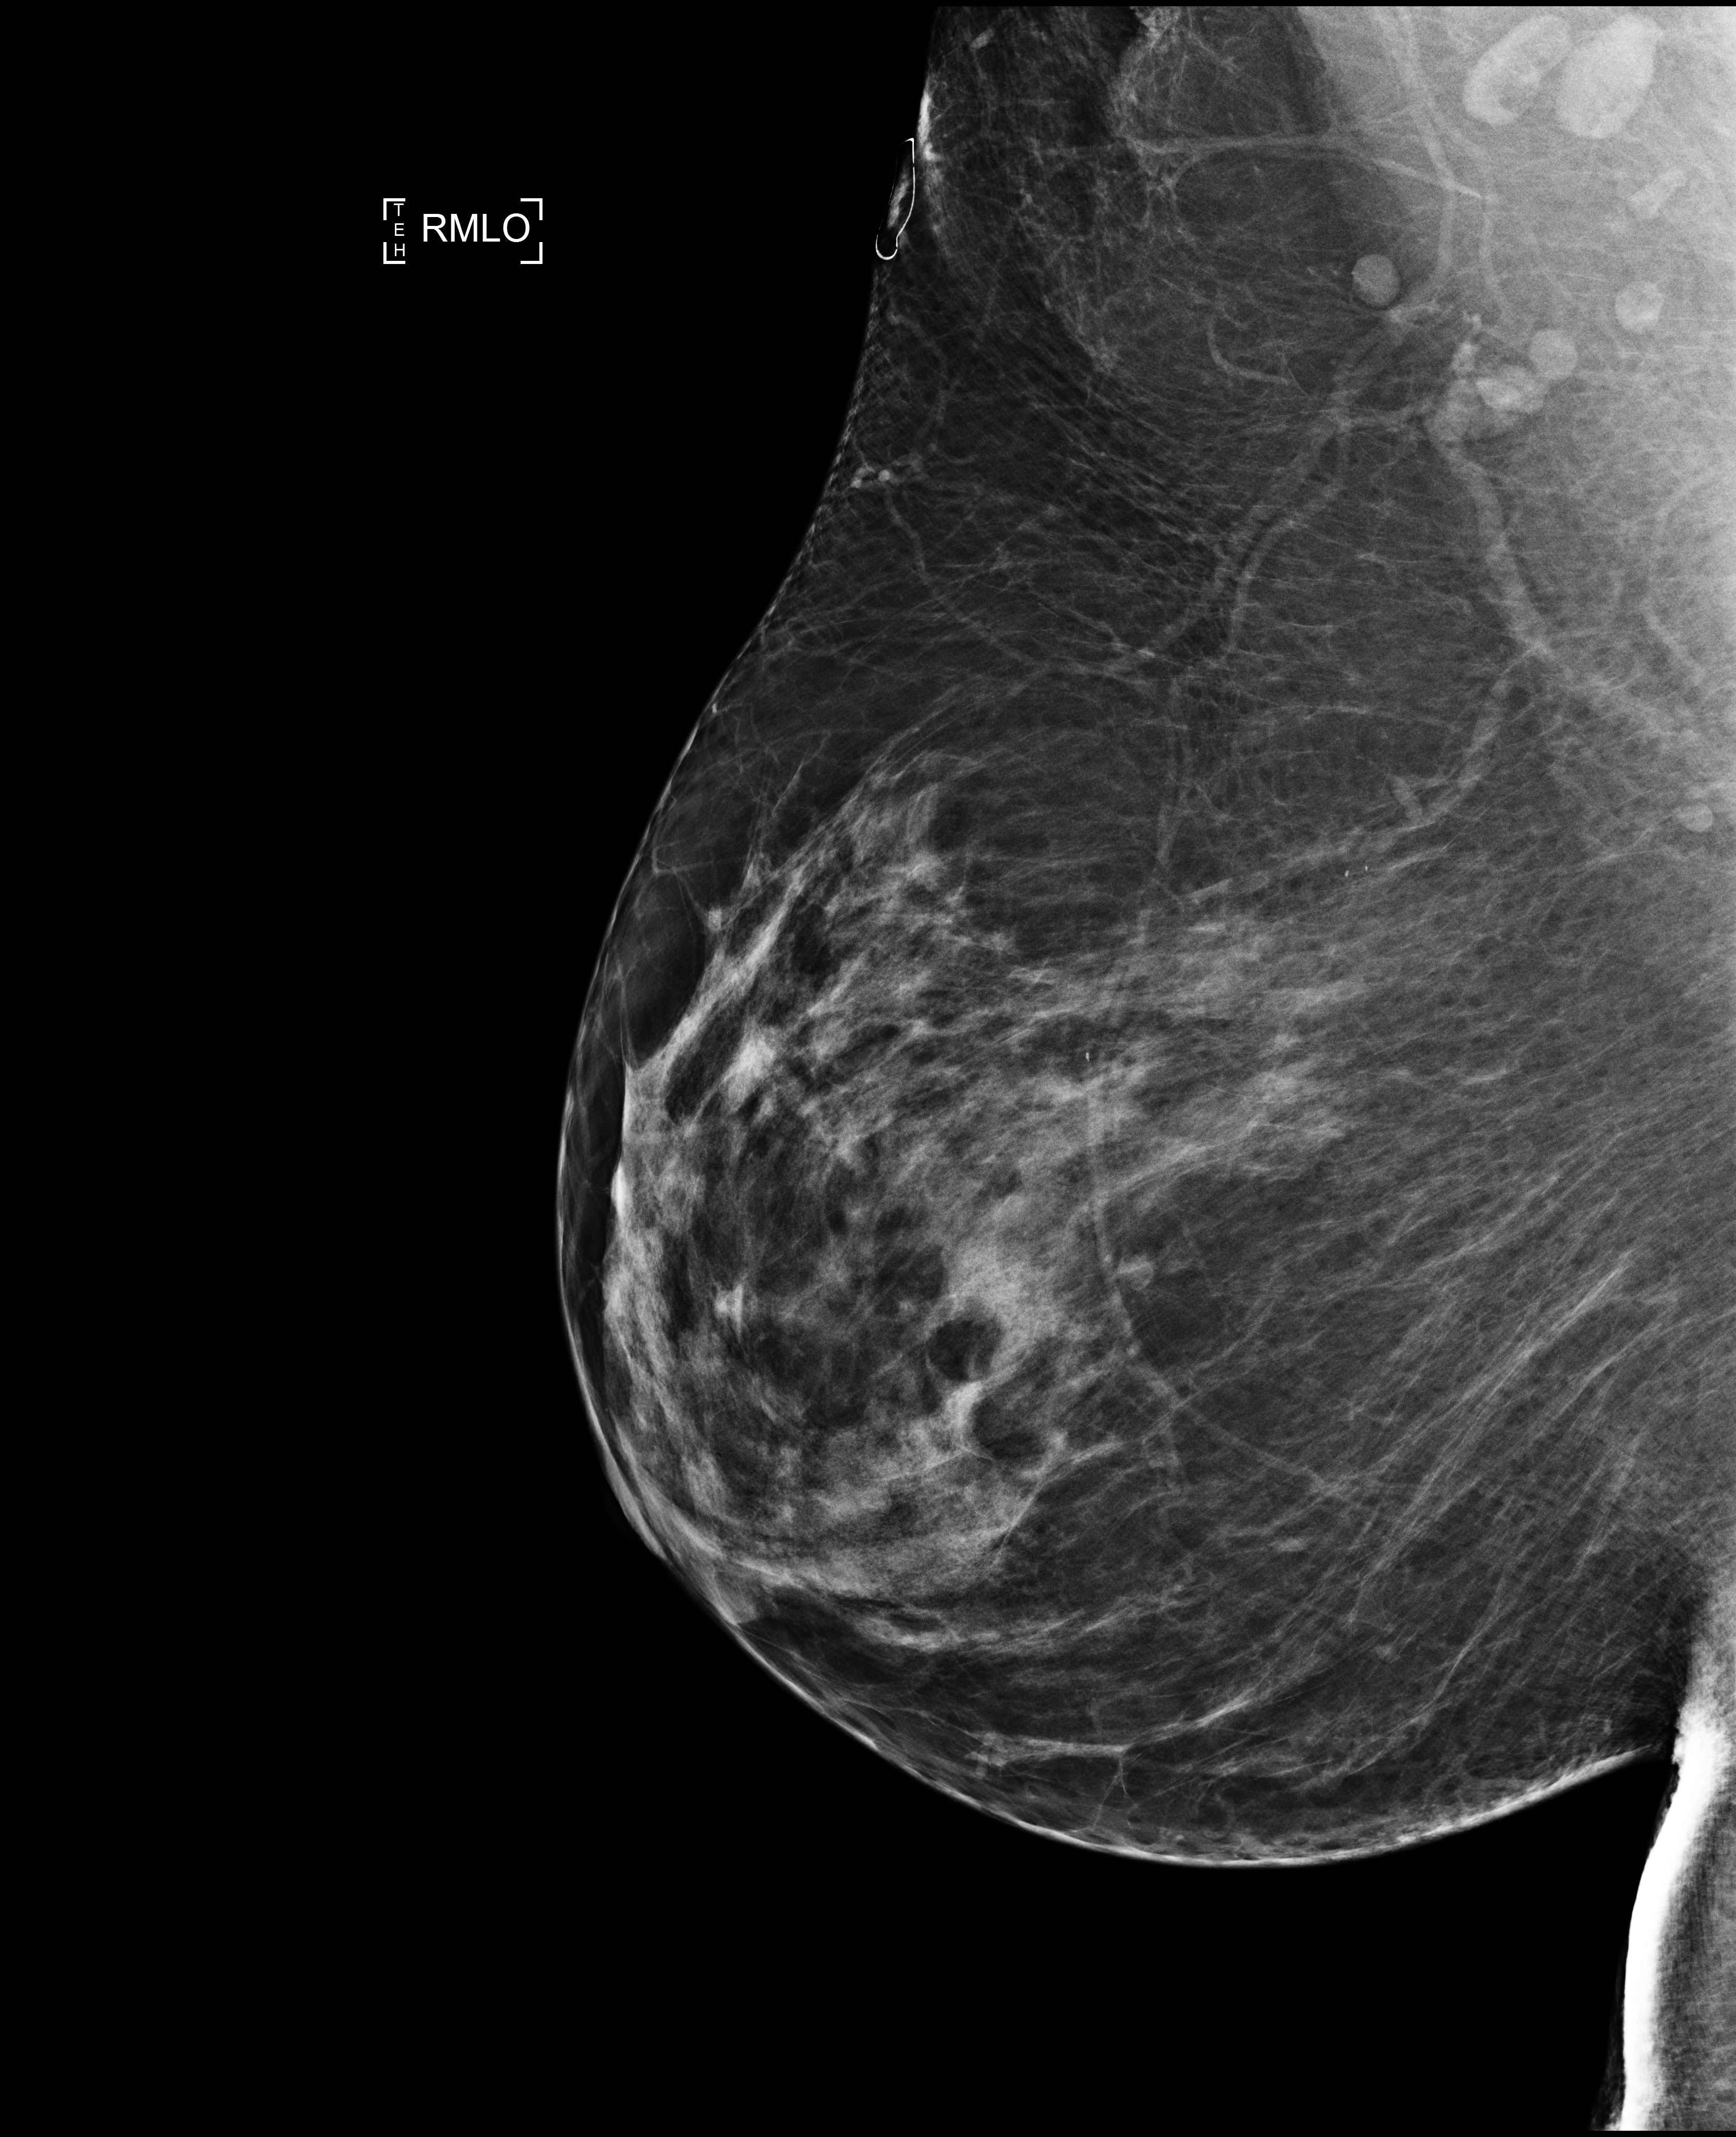
Screening examination; compressed breast thickness 90 mm. Patient aged 65 years (female).
Image type: full-field digital mammogram. Breast: right. Projection: medio-lateral oblique projection.